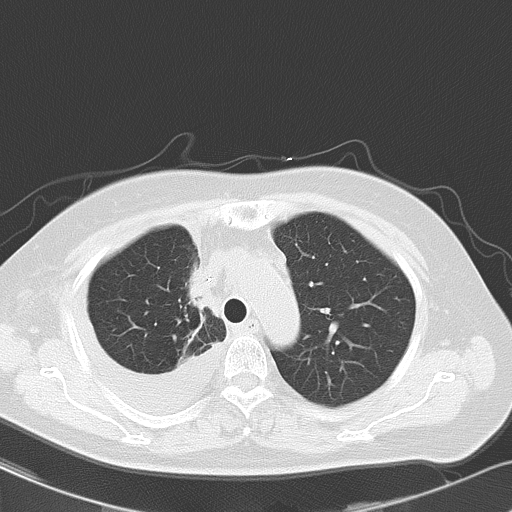
Chest CT, one axial slice. Slice 38 of 48 in the series (ordered by position). Reconstruction kernel B70f. 120 kVp. Lung window (W 1500 / L -600 HU). 5 mm slice thickness. 512 × 512 image matrix, field of view 328 × 328 mm. Female patient, age 69 years. From the clinical record (not read from this slice): clinical TNM (as recorded): T2a N0 M1c.
Outlined on this slice (bounding box drawn by a radiologist):
- lung tumour (recorded histology: adenocarcinoma): bounding box [x1, y1, x2, y2] px = [176, 247, 216, 322]